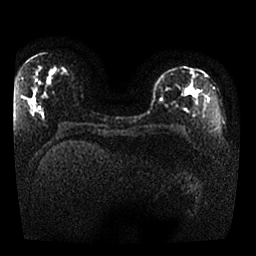
Breast MRI, one axial slice. Position 12 of 25 along the scan axis. Diffusion-weighted series; image 2 of 4 stored at this slice position (different b-values; order by instance number). 1.5 T. 4 mm slice thickness. 256 × 256 image matrix, field of view 330 × 330 mm. Female patient.
Annotated regions visible in this slice (expert manual segmentation):
- tumour on diffusion-weighted imaging: bounding box <158,96,164,102> (left, top, right, bottom; pixels)